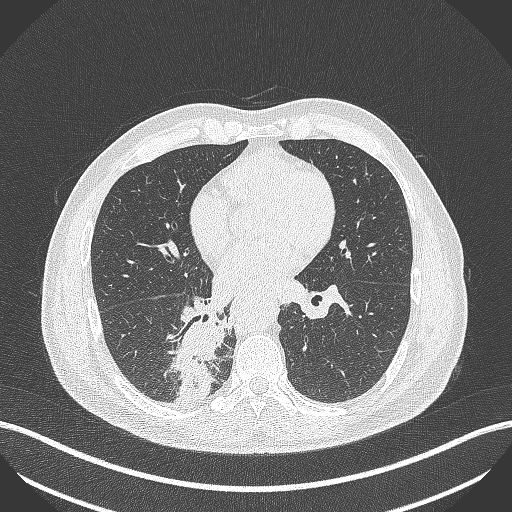
Chest CT, one axial slice; slice 219 of 451 in the series (ordered by position); reconstruction kernel B70f; lung window (W 1500 / L -600 HU); 1 mm slice thickness; 512 × 512 image matrix. Patient: male, 61 years. Case-level facts recorded for this patient, not image findings: clinical TNM (as recorded): T1 N0 M0.
Outlined on this slice (rectangle marked by the reading radiologist):
- lung tumour (recorded histology: small cell carcinoma): bounding box (x1, y1, x2, y2) in pixels: (169, 315, 226, 415)